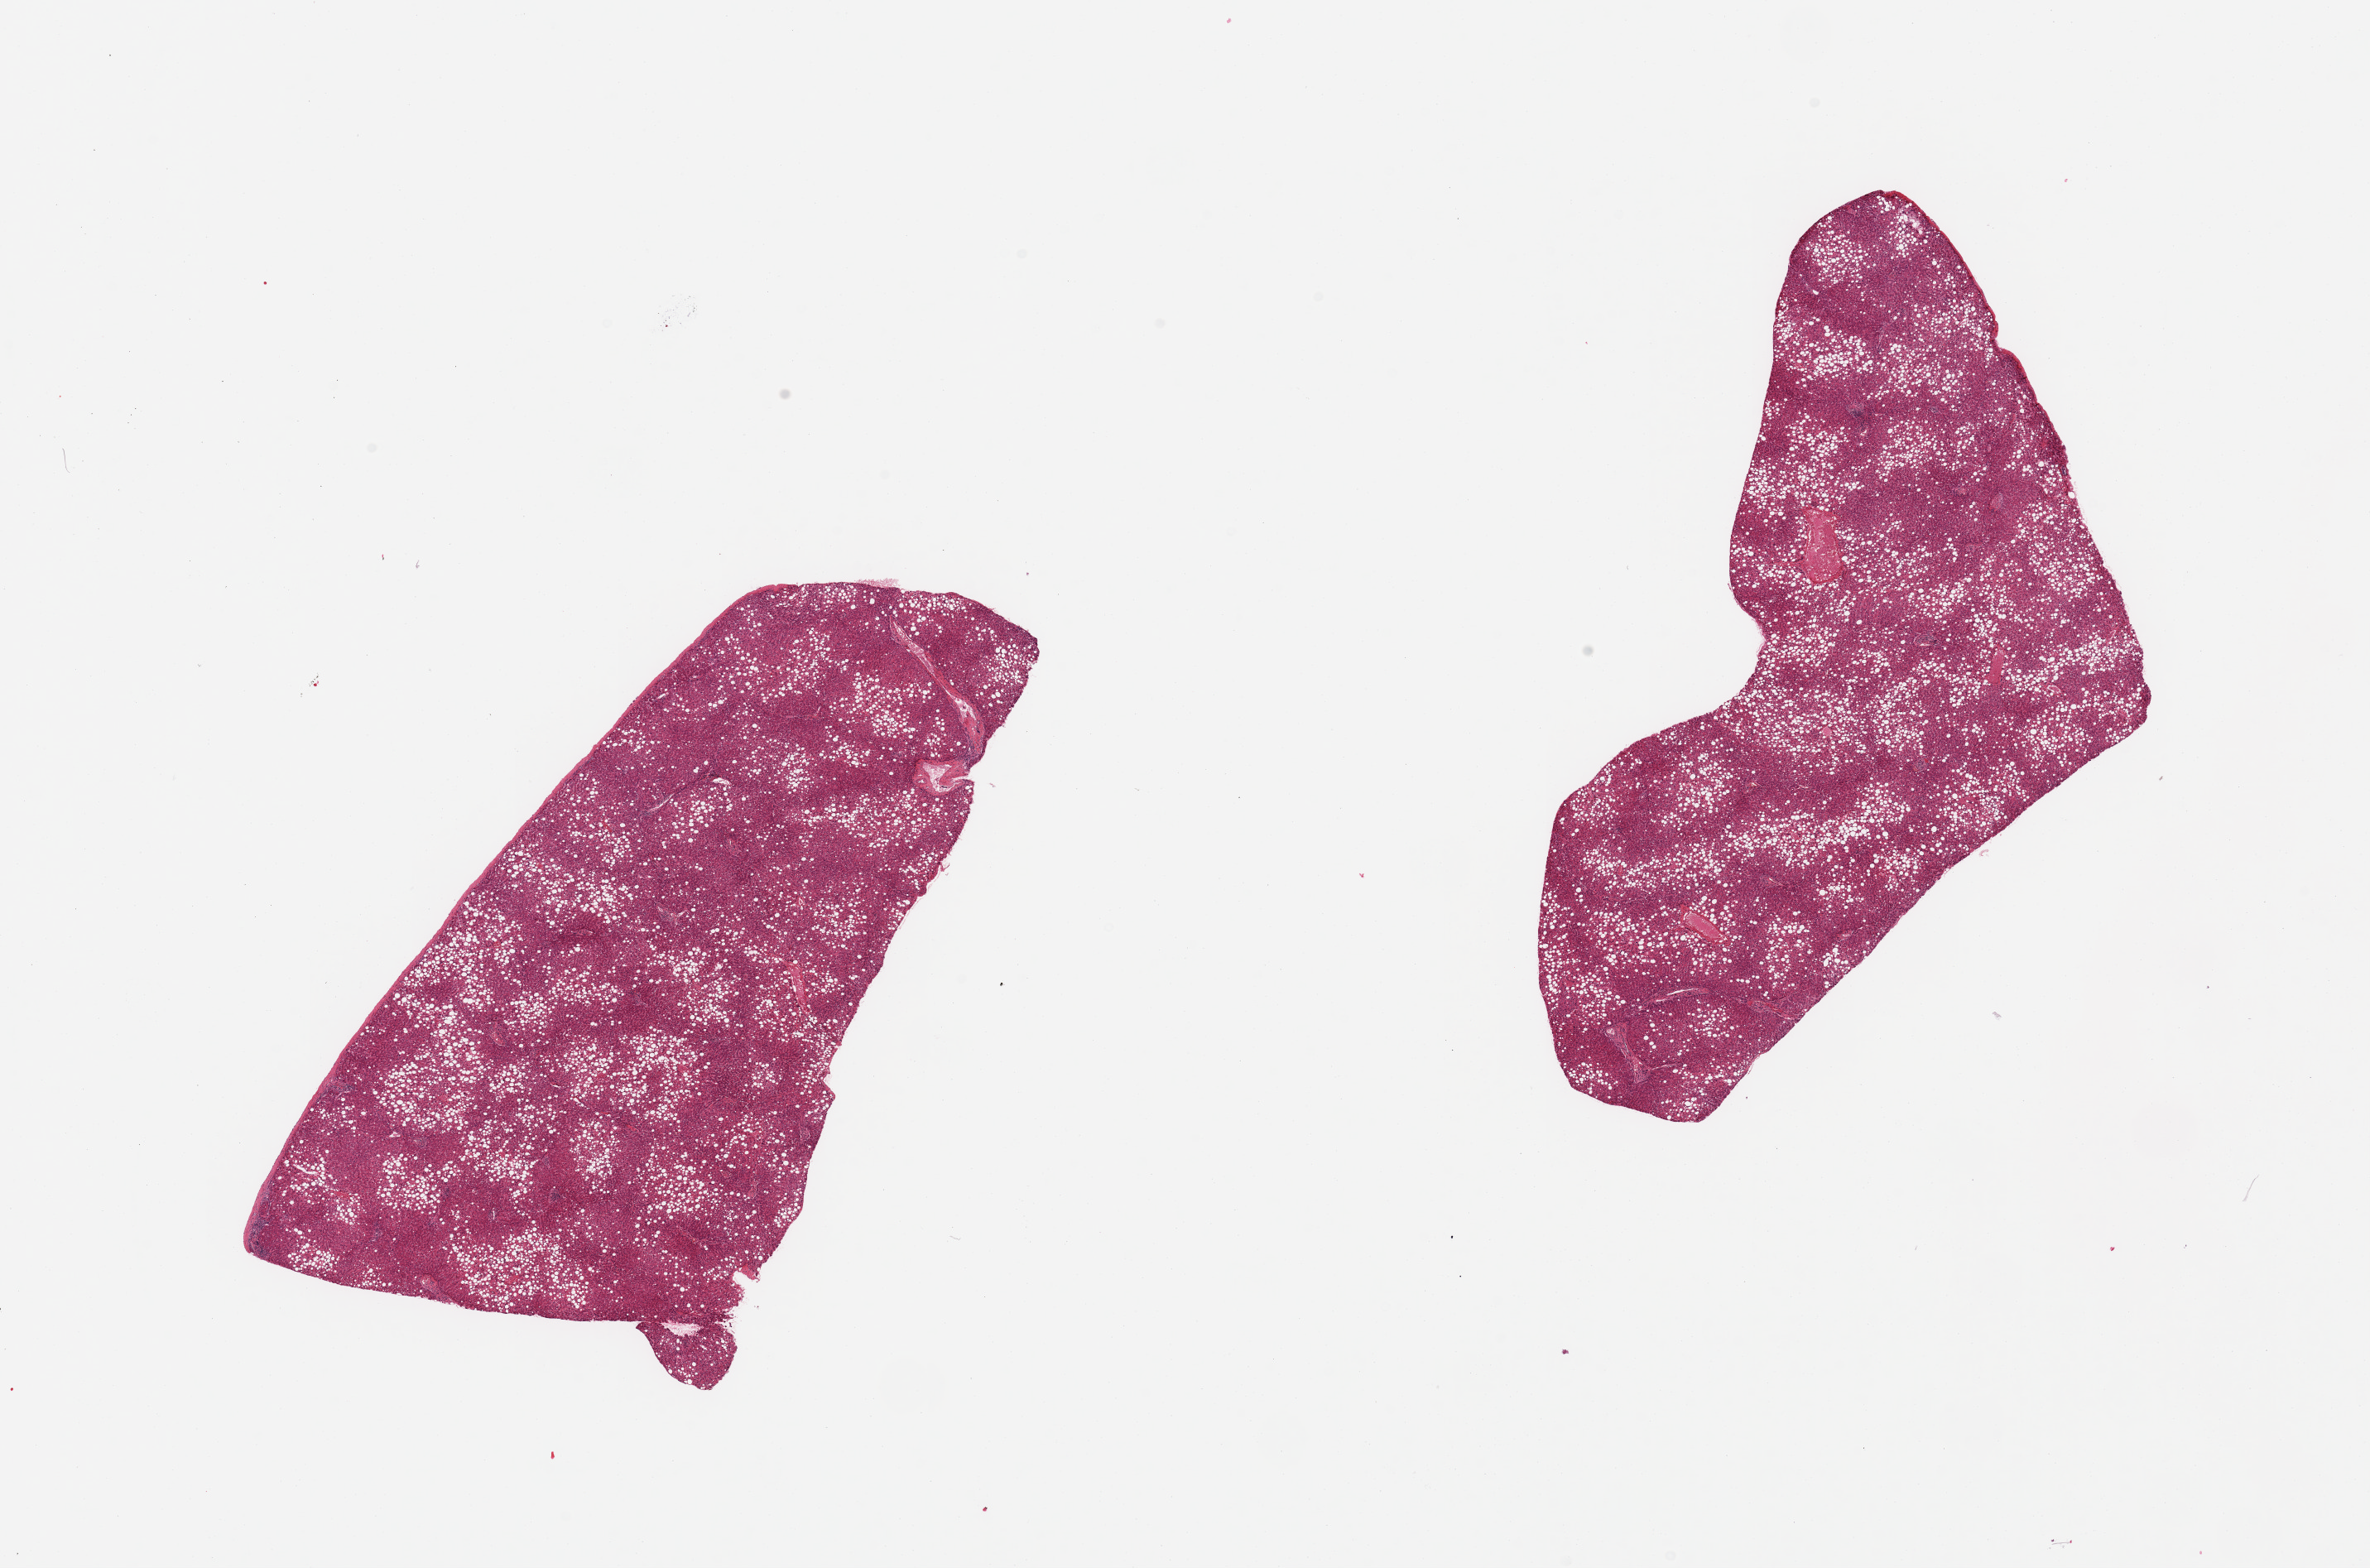
Haematoxylin and eosin whole-slide image — a low-resolution overview of the entire scanned area, about 22.6 x 15.0 mm (slide scanned at 20x); PAXgene-fixed paraffin-embedded (PFPE) section; section of liver (target tissue); donor tissue sample.
Reviewer comment on this tissue sample: 2 pieces; severe (>75%) macrovesicular steatosis.